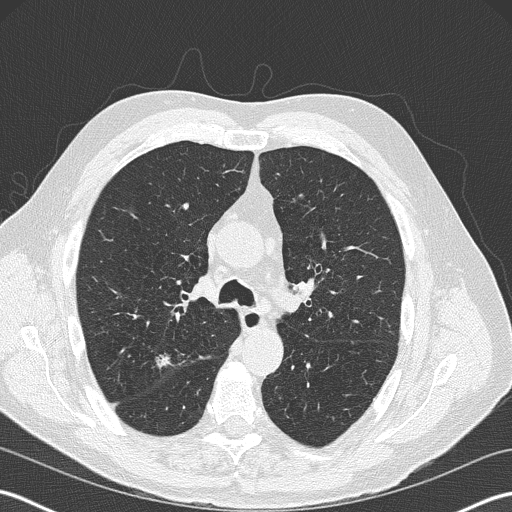
Low-dose screening chest CT, one axial slice. Slice 126 of 199 in the series (ordered by position). Reconstruction kernel B50f. 120 kVp. Lung window (W 1500 / L -600 HU). 2 mm slice thickness. 512 × 512 image matrix, field of view 350 × 350 mm.
Outlined on this slice (outlined manually by an expert reader):
- lesion 1 (tumor, upper lobe of right lung): bounding box <153,350,174,371> (left, top, right, bottom; pixels)